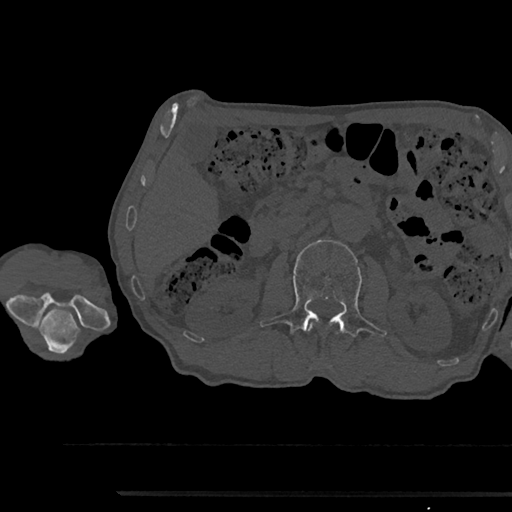
CT including the spine, one axial slice. Slice 576 of 797 in the series (ordered by position). Reconstruction kernel Br40s/3. Bone window (W 1800 / L 400 HU). 0.5 mm slice thickness. 512 × 512 image matrix, field of view 367 × 367 mm. Male patient, age 79 years. From the clinical record (not read from this slice): primary cancer: prostate.
Structures marked on this image (semi-automatically segmented with operator editing):
- L1 vertebra: bounding box (x1, y1, x2, y2) in pixels: (309, 324, 313, 329)
- L2 vertebra: (260, 240, 387, 363)